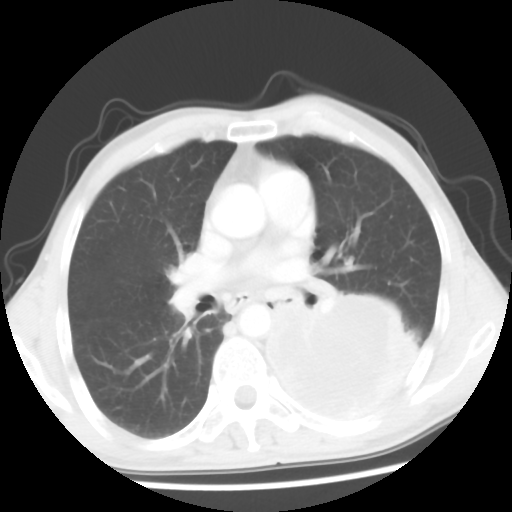
Chest CT, one axial slice; slice 31 of 56 in the series (ordered by position); reconstruction kernel STANDARD; 120 kVp; lung window (W 1500 / L -600 HU); 512 × 512 image matrix, field of view 318 × 318 mm. Male patient, age 60 years. From the clinical record (not read from this slice): clinical TNM (as recorded): T4 N0 M0.
Annotated regions visible in this slice (bounding box drawn by a radiologist):
- lung tumour (recorded histology: squamous cell carcinoma): box from (x=243, y=286) to (x=422, y=422) px